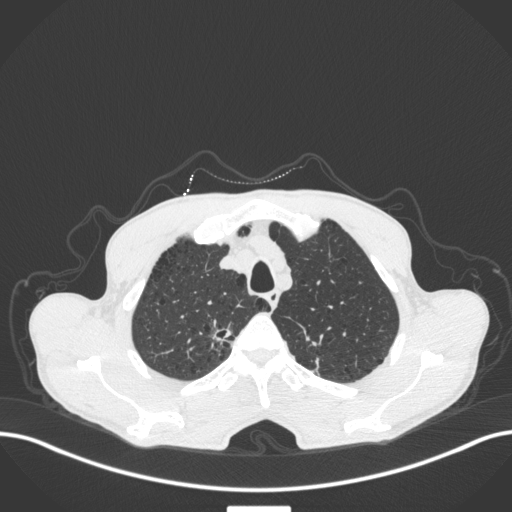
Chest CT, one axial slice. Position 361 of 445 along the scan axis. 120 kVp. Lung window (W 1500 / L -600 HU). 1 mm slice thickness. 512 × 512 image matrix, field of view 400 × 400 mm. Patient: male, 70 years. Case-level facts recorded for this patient, not image findings: clinical TNM (as recorded): T1a N0 M0.
Annotated regions visible in this slice (bounding box drawn by a radiologist):
- lung tumour (recorded histology: adenocarcinoma): bounding box (x1, y1, x2, y2) in pixels: (206, 318, 233, 348)